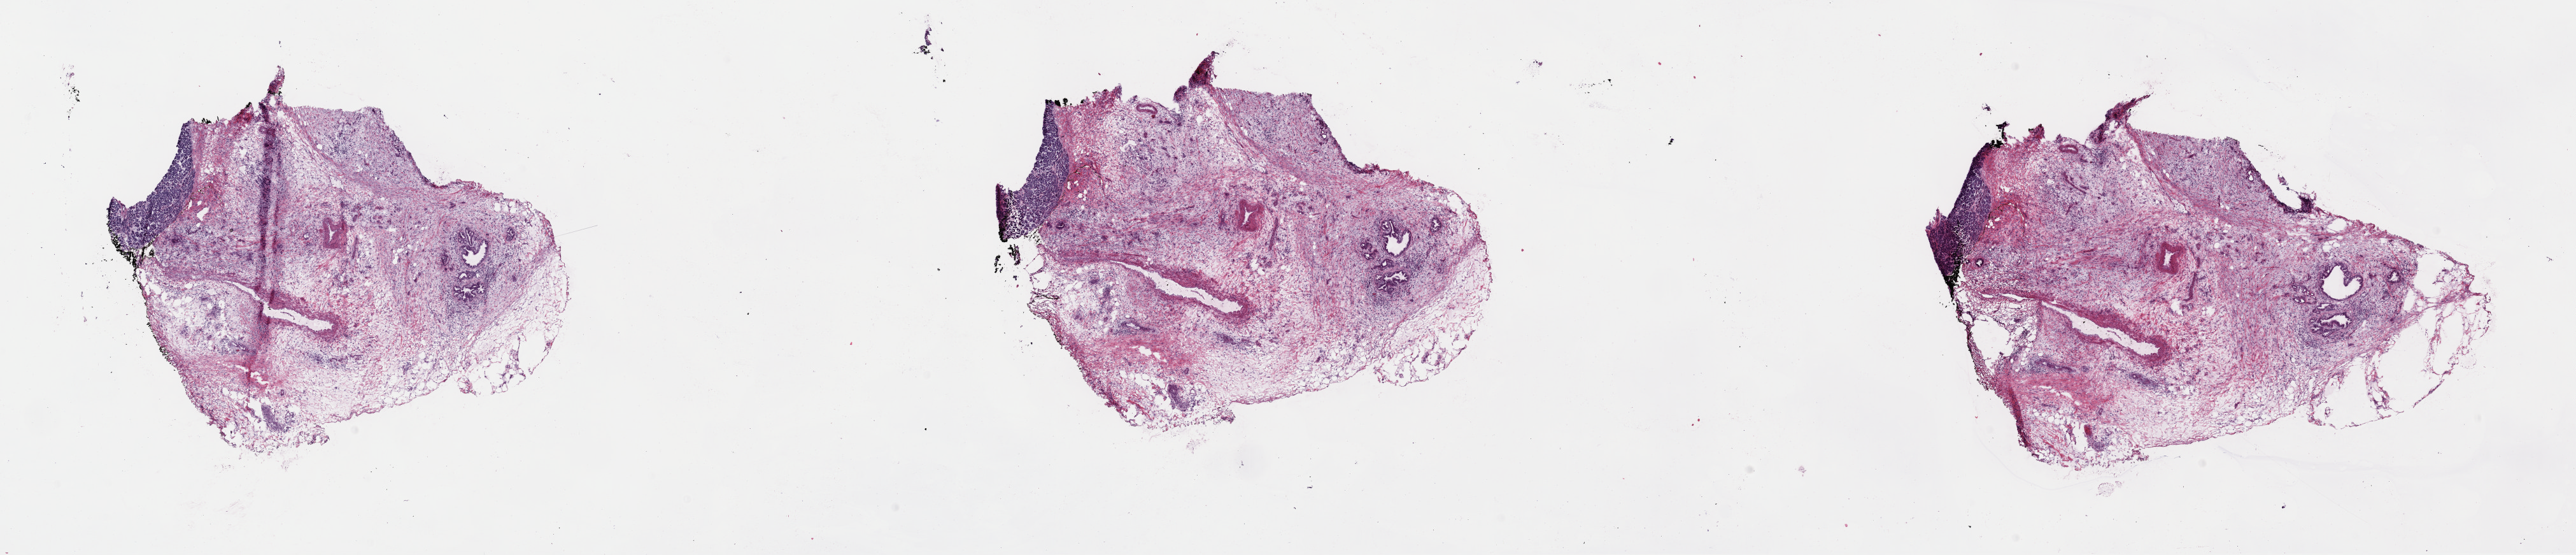
H&E whole-slide image — a low-resolution overview of the entire scanned area, about 32.0 x 6.9 mm; frozen section from the top of the tissue portion; pancreas, primary tumour sample. Patient: female, age at initial diagnosis 68 years. Histologic grade: G2 (moderately differentiated). Slide review estimates, as recorded: tumour cells 10%, tumour nuclei 10%, normal cells 20%, stromal cells 70%, necrosis 0%. Inflammatory infiltration, as recorded: lymphocyte infiltration 10%, monocyte infiltration 0%, neutrophil infiltration 1%.
AJCC pathologic stage: IIB (7th edition). Pathologic diagnosis: Infiltrating duct carcinoma, NOS (head of pancreas).